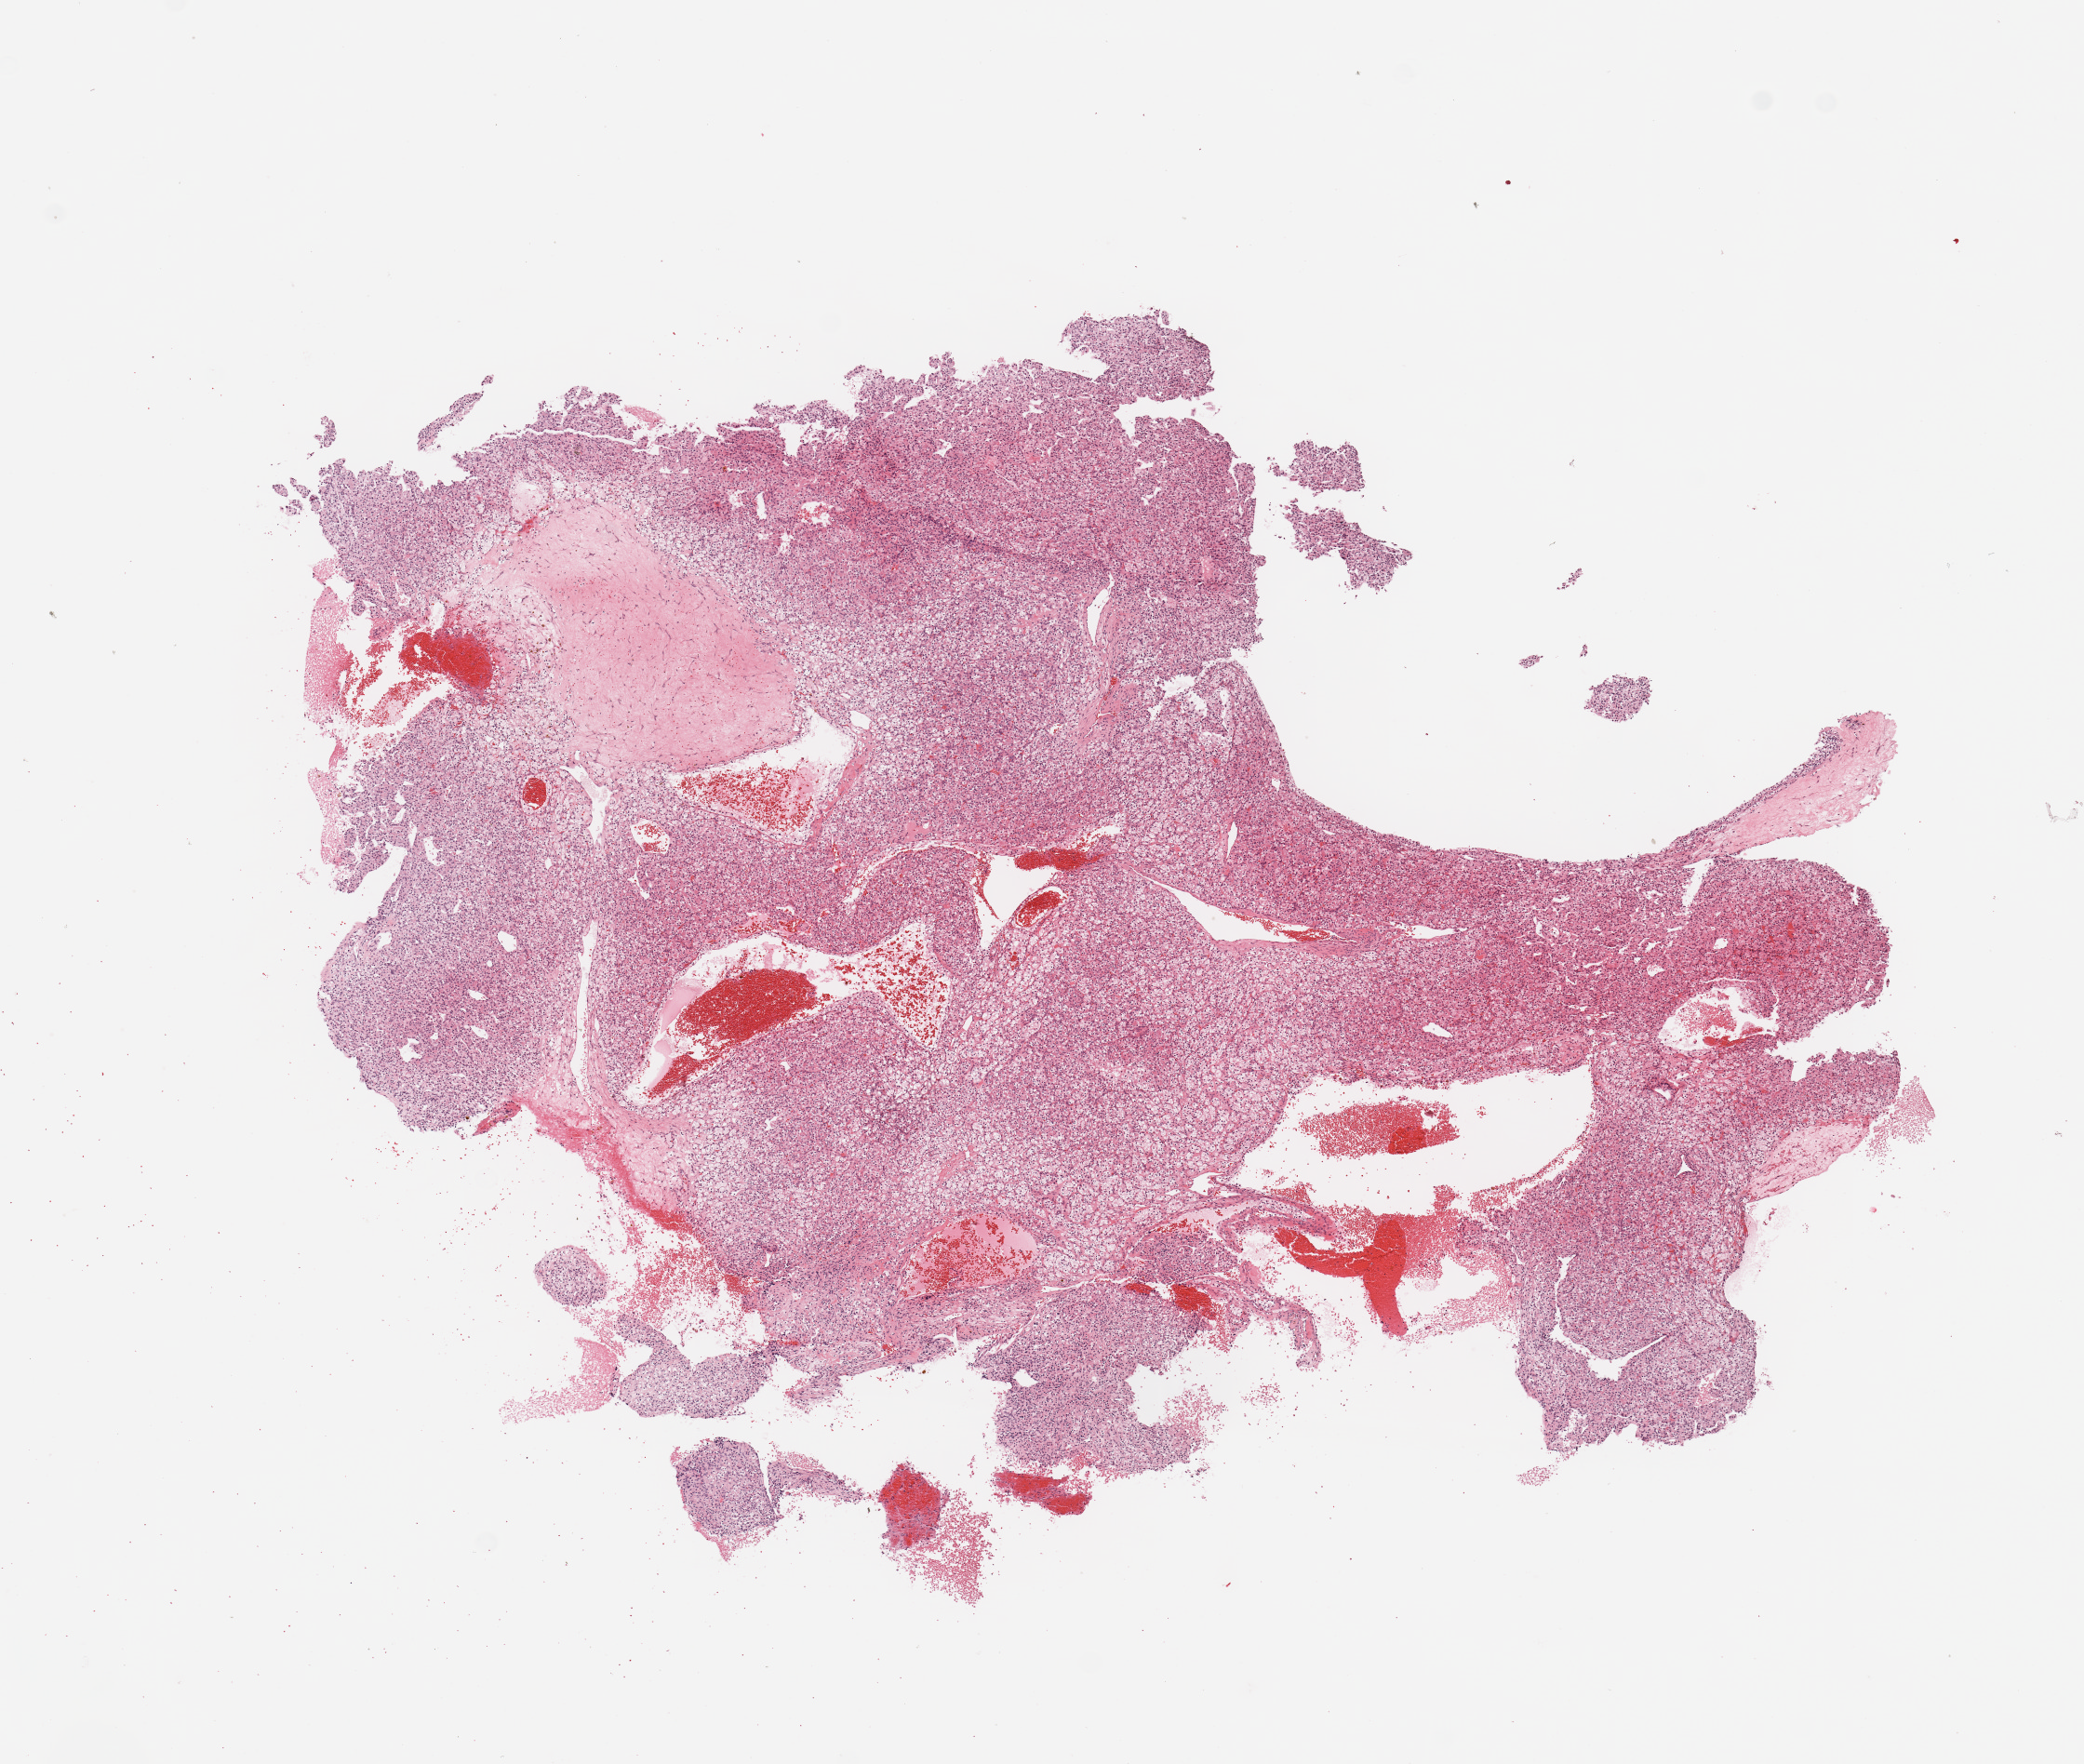
Whole-slide histology image, H&E-stained — shown as a low-resolution overview of the whole scanned area (about 8.9 x 7.5 mm); tumour tissue sample, sampled site: kidney. Patient: female, age 31 years. Histologic grade: G2 (moderately differentiated). Slide review estimates, as recorded: tumour nuclei 90%, necrosis 5%.
* primary tumour site (as recorded): upper pole
* diagnosis: Renal cell carcinoma, NOS
* AJCC pathologic stage: I